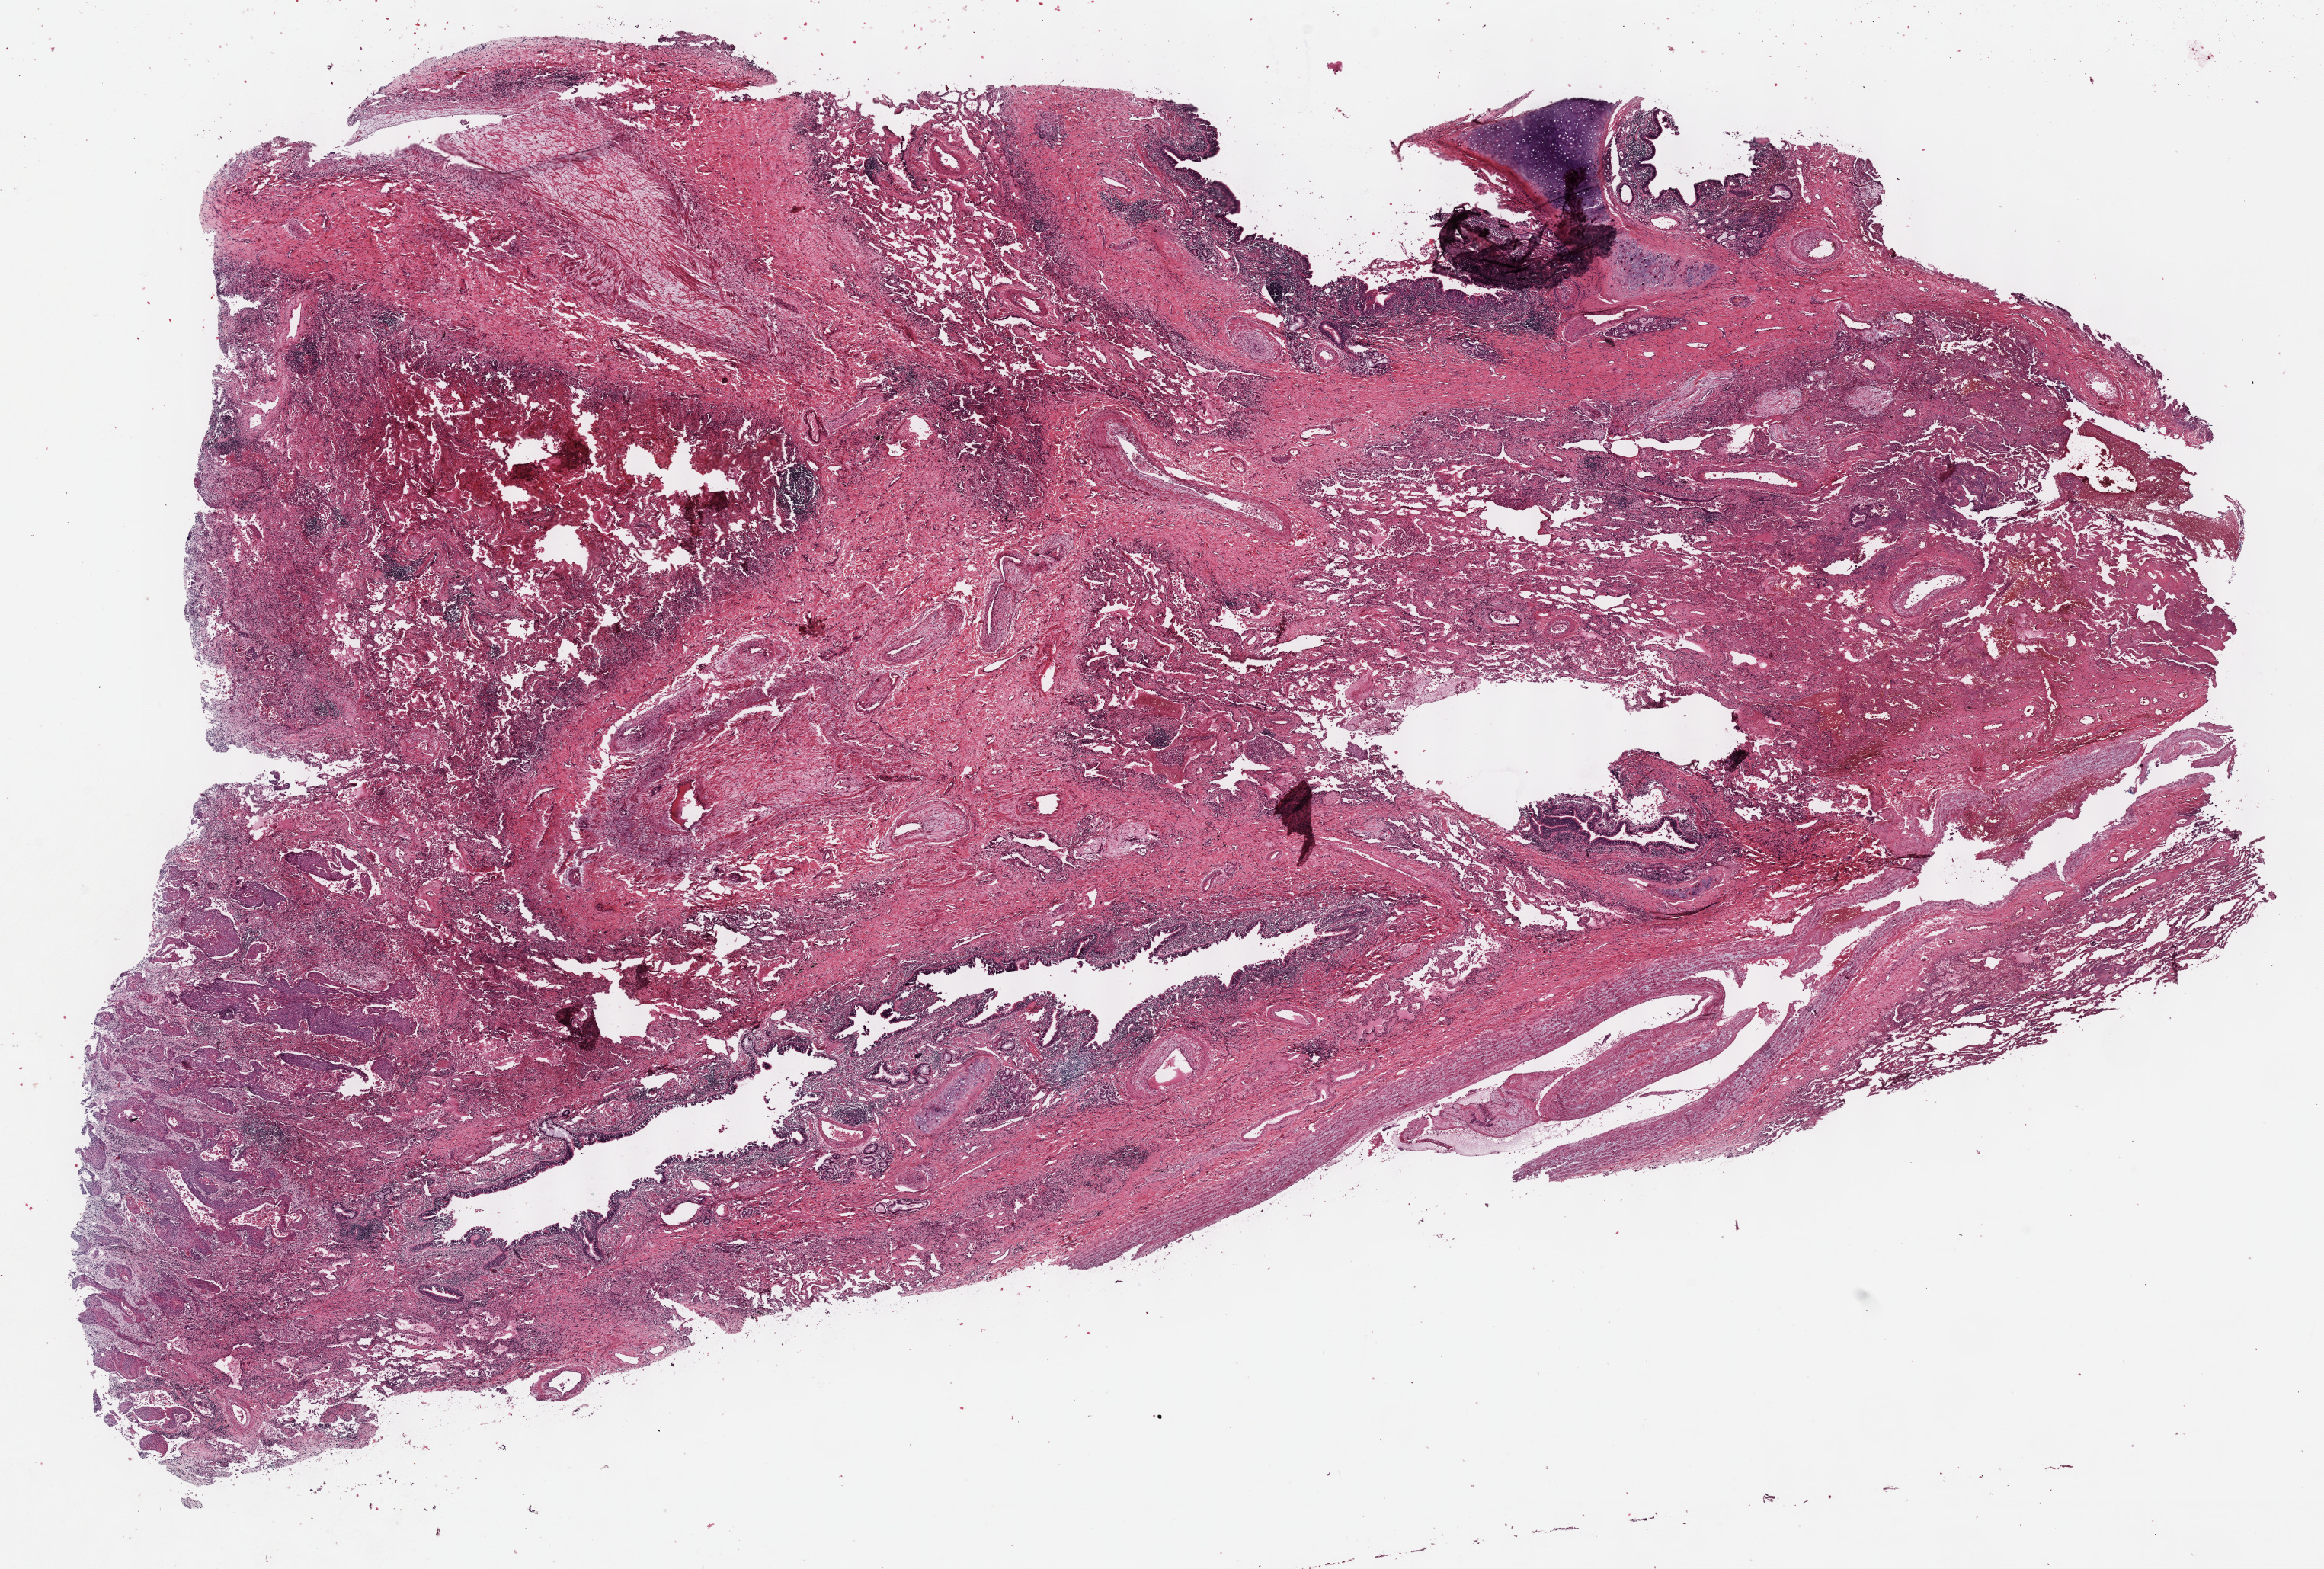
Digitized H&E-stained tissue section (whole slide), shown as a low-resolution overview of the whole scanned area (about 24.7 x 16.7 mm), FFPE section, primary tumour sample from the lung. Female patient; age at initial diagnosis 75 years.
- AJCC pathologic stage: II (6th edition)
- histologic diagnosis: Squamous cell carcinoma, NOS (upper lobe, lung)